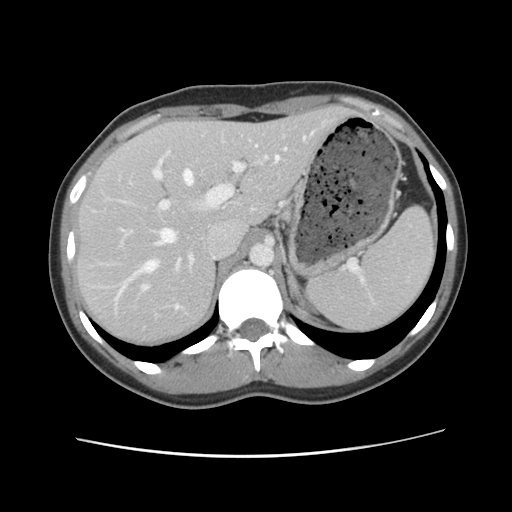
Contrast-enhanced abdominal CT, one axial slice; slice 78 of 134 in the series (ordered by position); soft-tissue window (W 400 / L 40 HU); 512 × 512 image matrix, field of view 339 × 339 mm. Female patient, age 33 years. From the clinical record (not read from this slice): diagnosis: colorectal cancer liver metastases, imaged before liver resection; multiple liver metastases: yes; largest metastasis: 4.5 cm; disease in both lobes: yes.
Structures marked on this image (outlined manually by an expert reader):
- hepatic veins: bounding box (x1, y1, x2, y2) in pixels: (122, 137, 306, 309)
- liver: (77, 108, 350, 346)
- planned liver remnant (the part of the liver to remain after resection): (78, 107, 351, 347)
- portal vein (with intrahepatic branches): (145, 139, 288, 288)